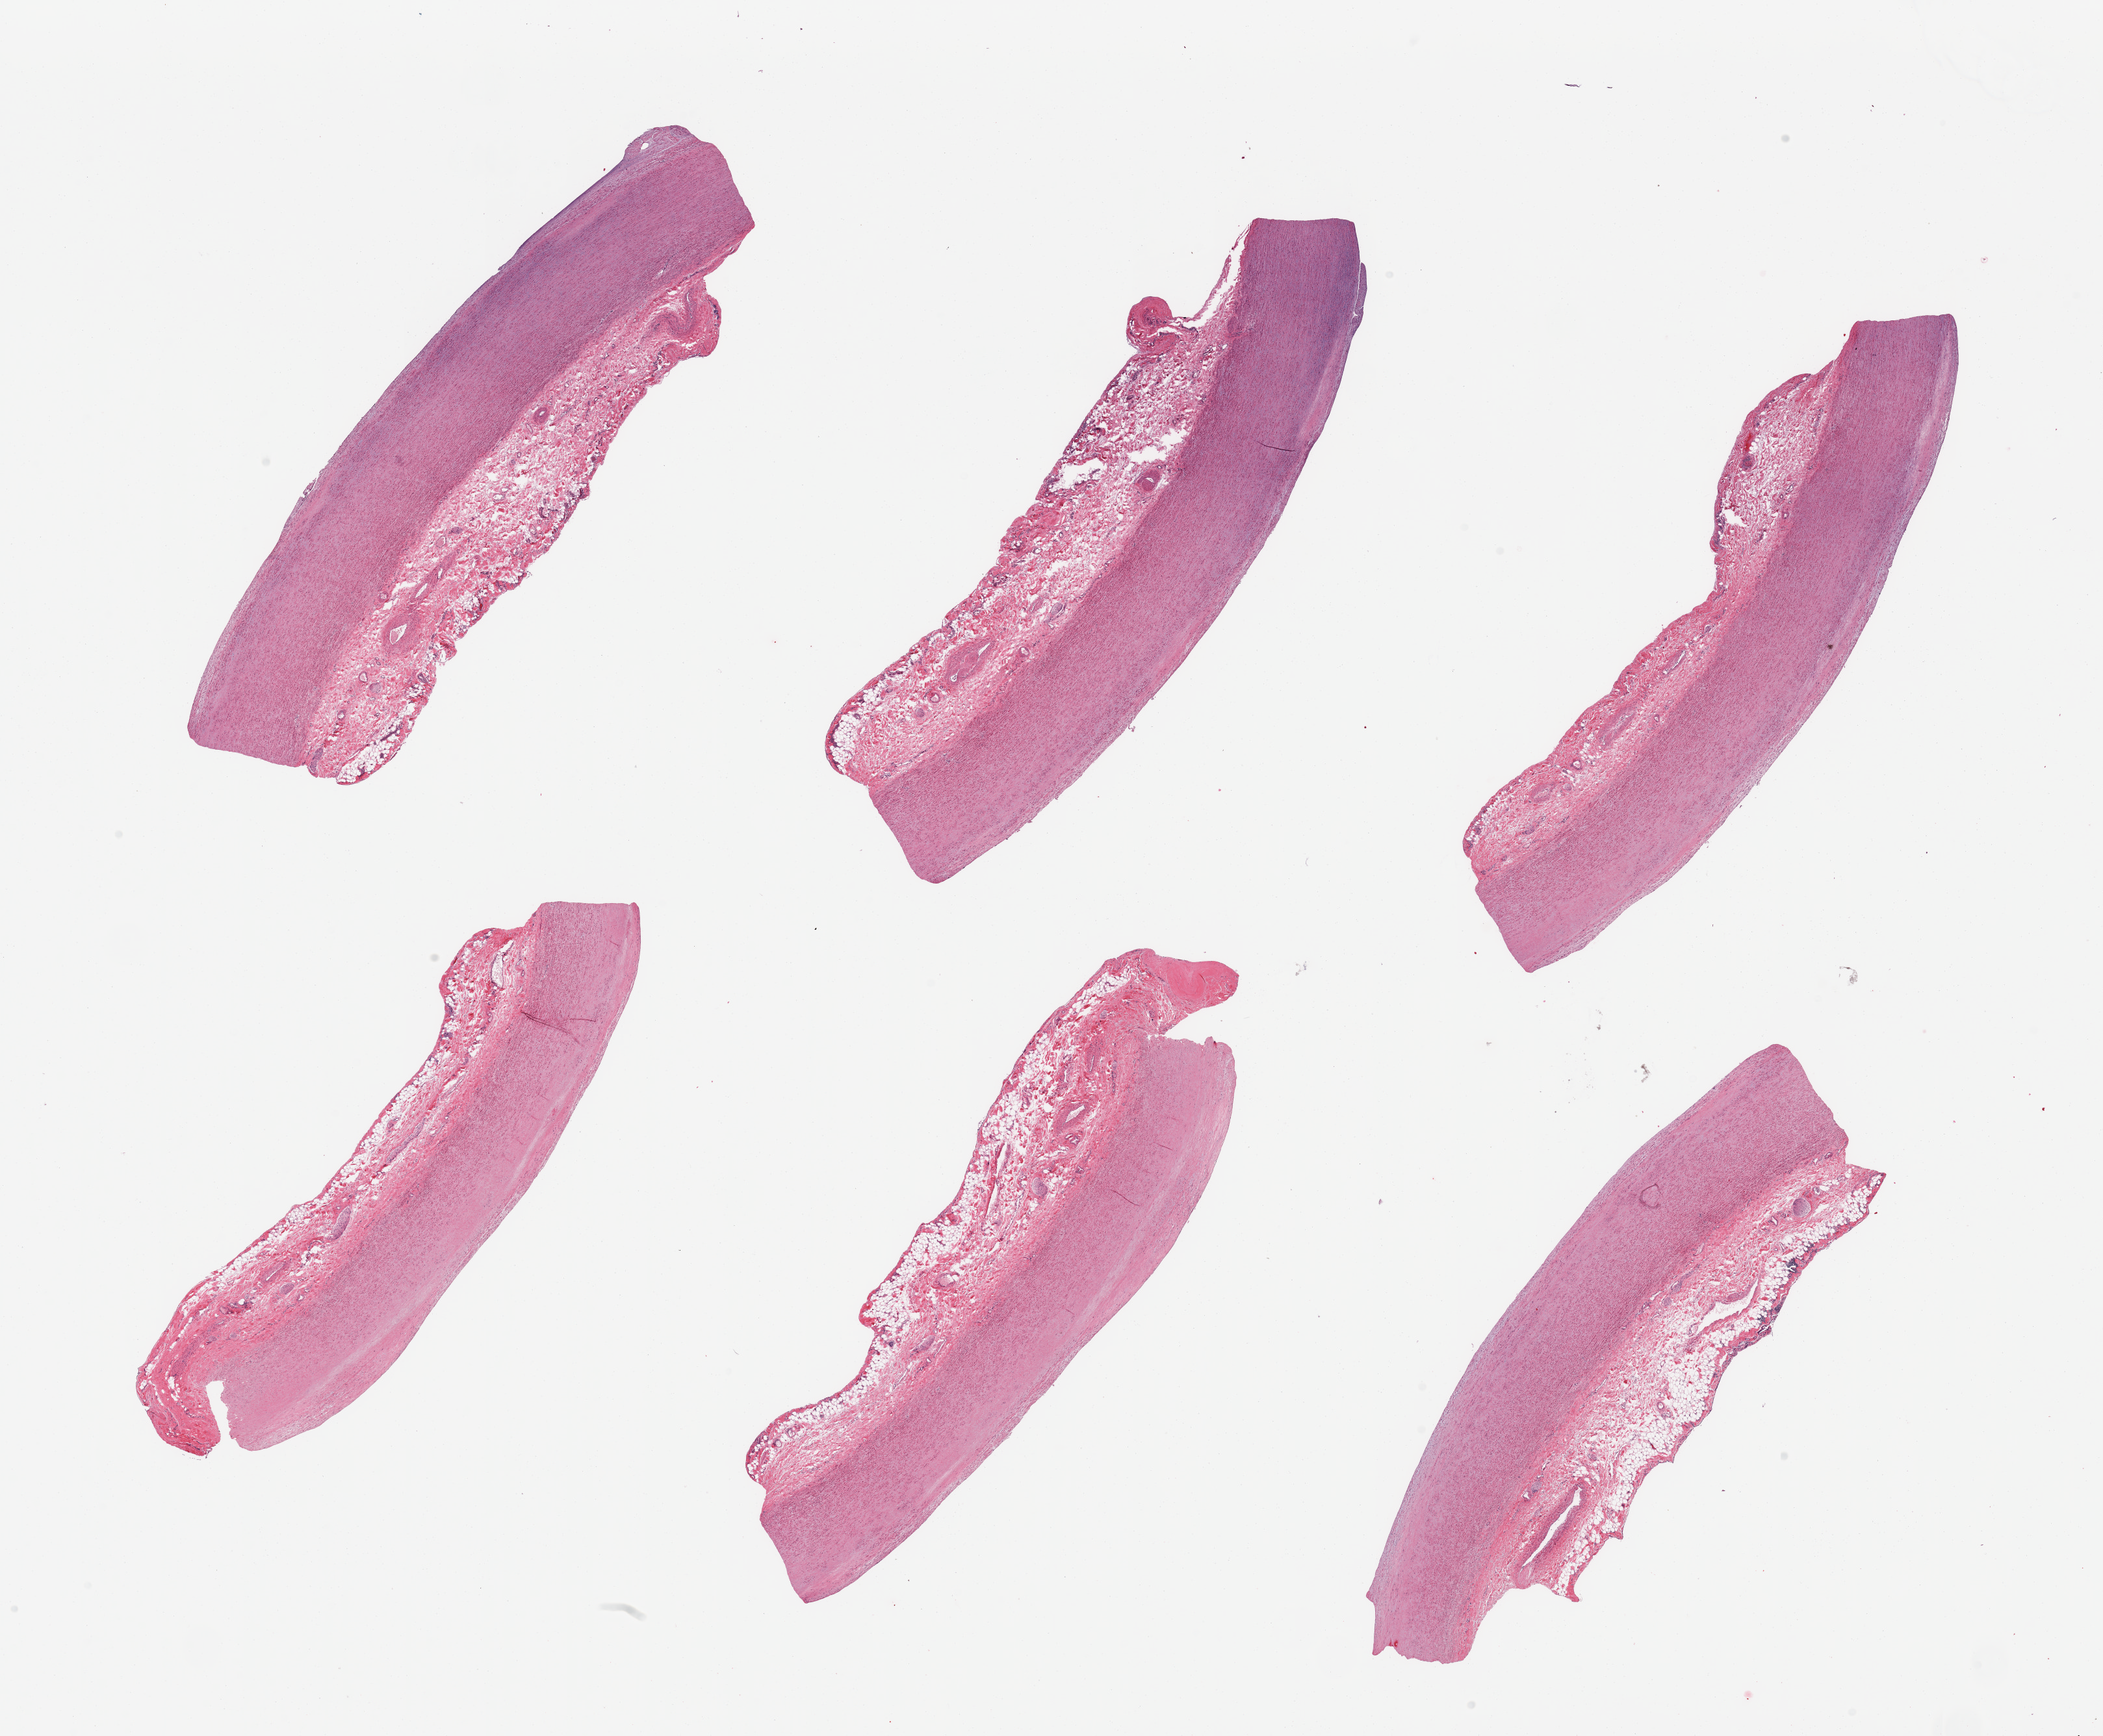
Whole-slide image, H&E stain — shown as a low-resolution overview of the whole scanned area (about 25.6 x 21.1 mm). PAXgene-fixed, paraffin-embedded tissue. Target tissue: aorta. Tissue donor sample. Donor sex: male.
• reviewer comment on this tissue sample: 6 pieces; thin flat fibrous plaques; untrimmed adventitia around 1mm thick